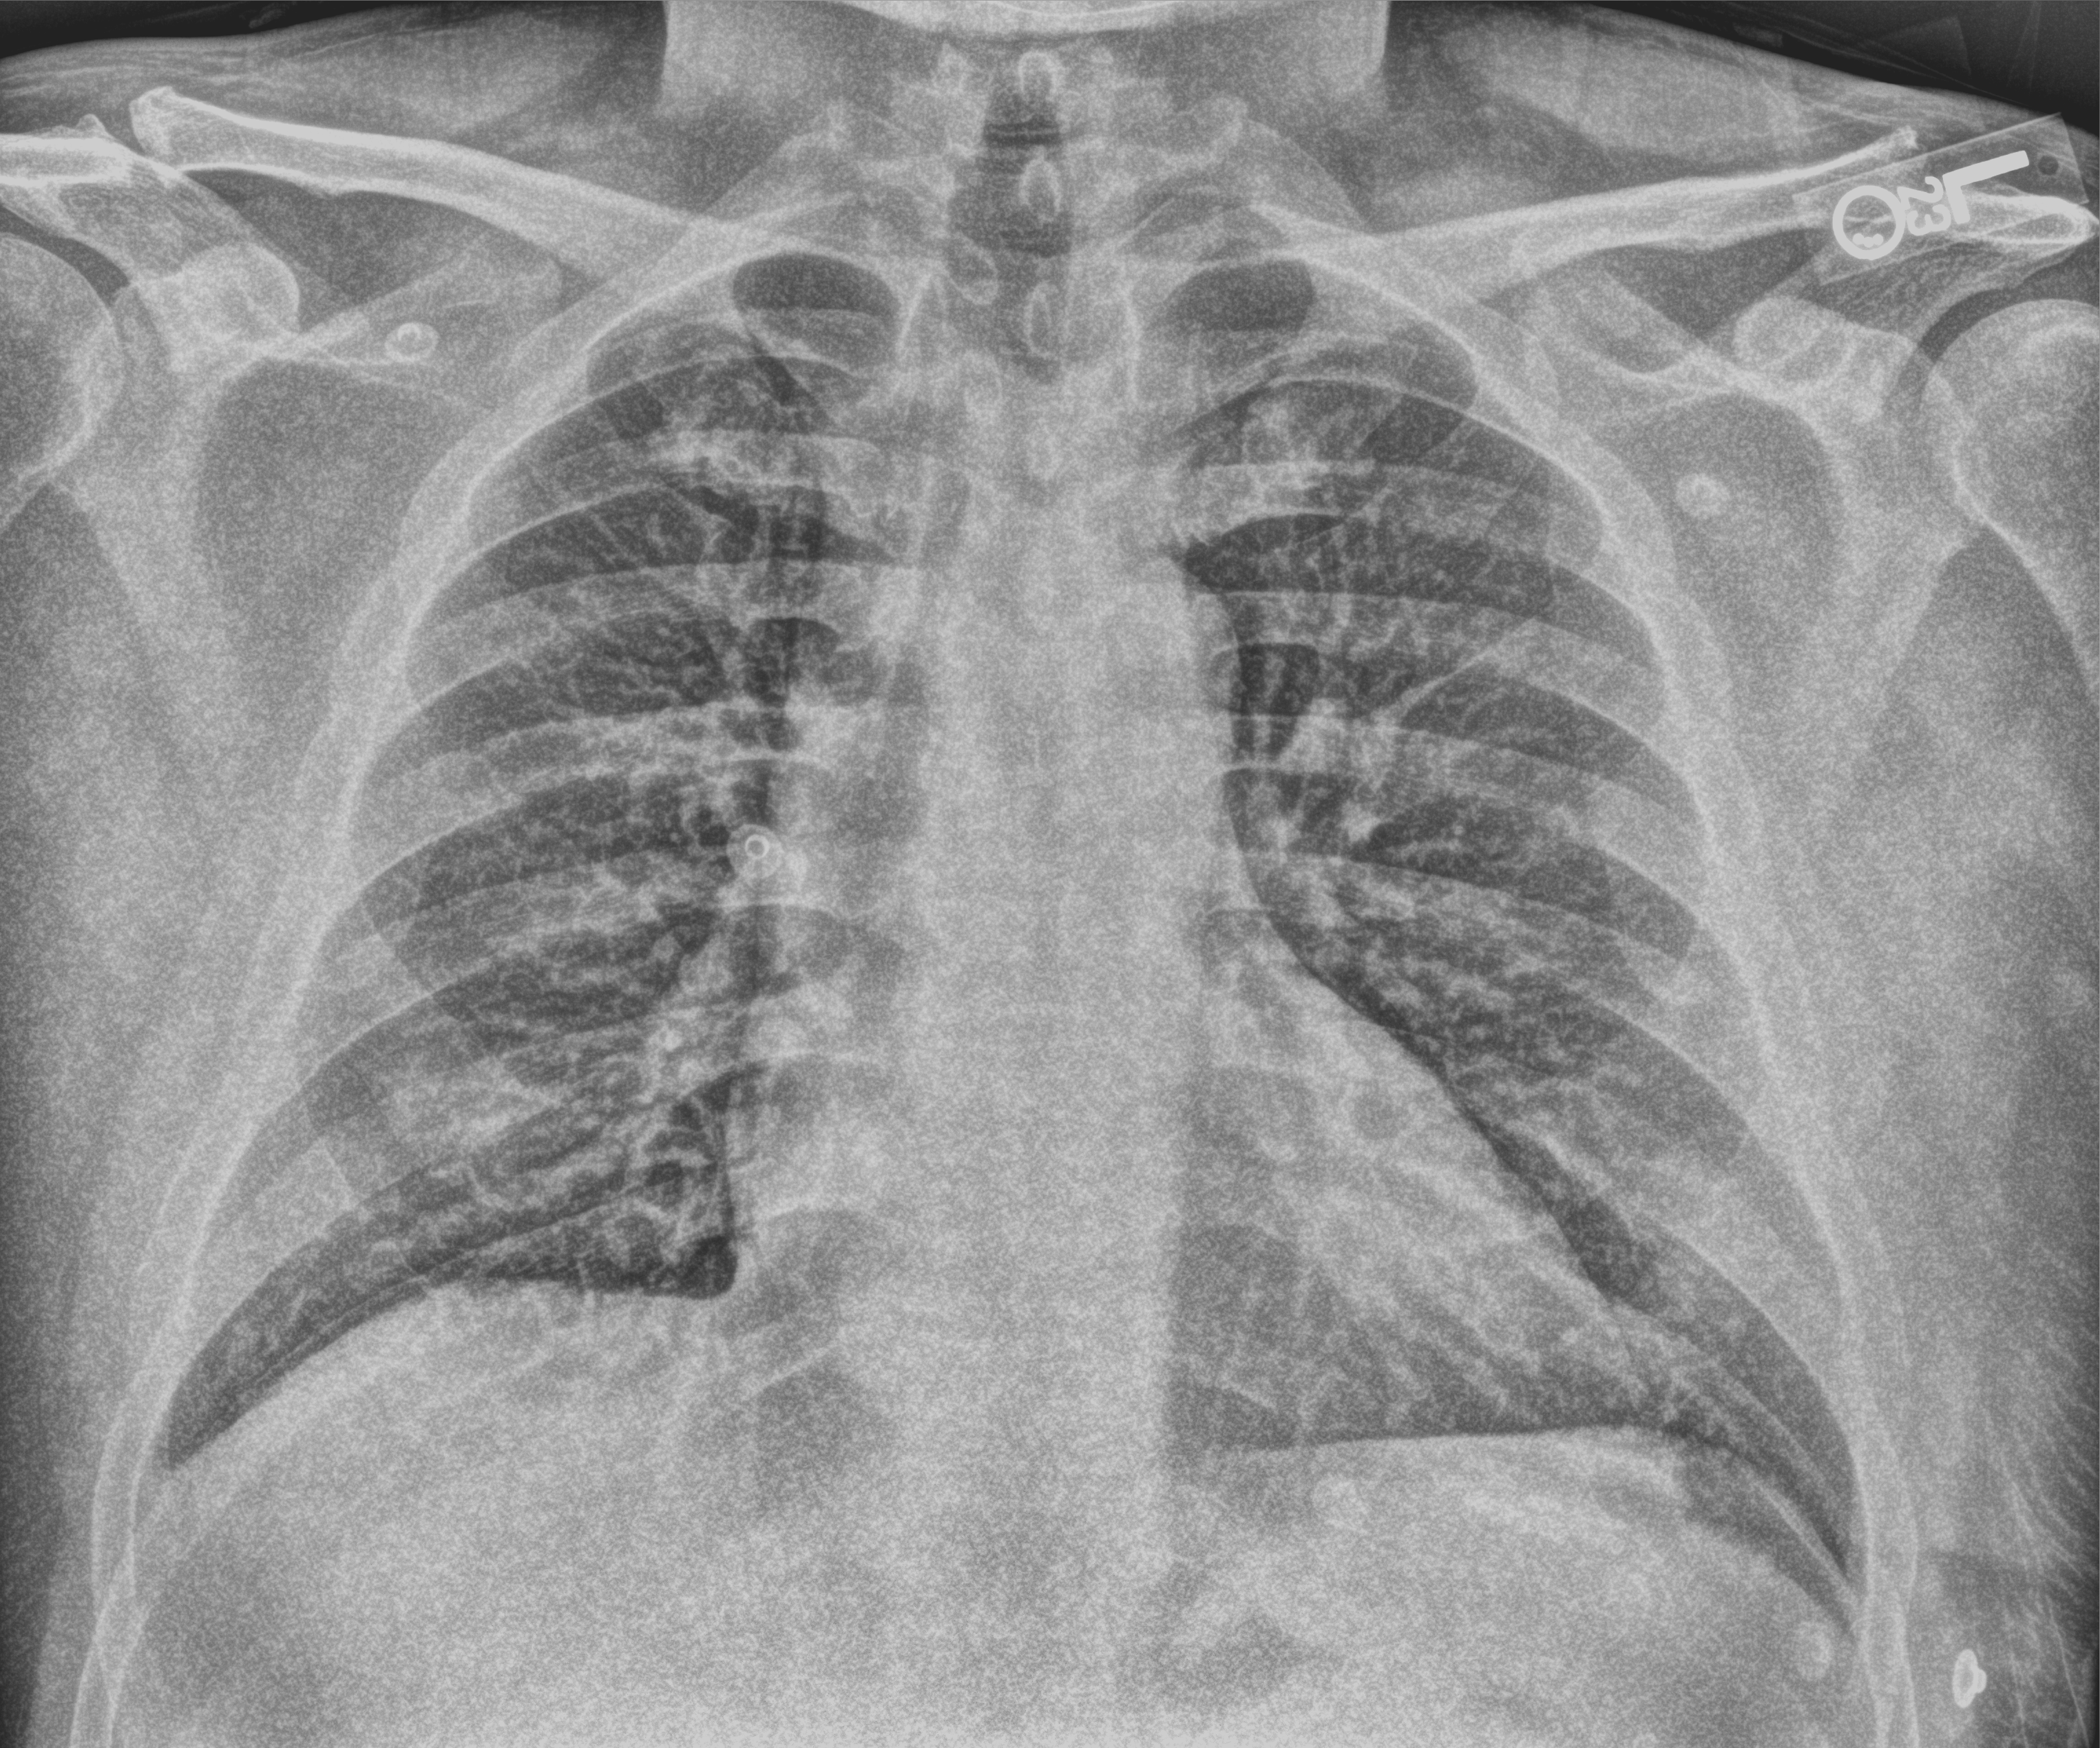
Portable chest radiograph; anteroposterior (AP) projection. Patient hospitalised with COVID-19; male, aged 18–59 years.
Admission-level facts for this patient (not findings on this image; timing relative to this image not recorded):
- length of hospital stay: 8 days